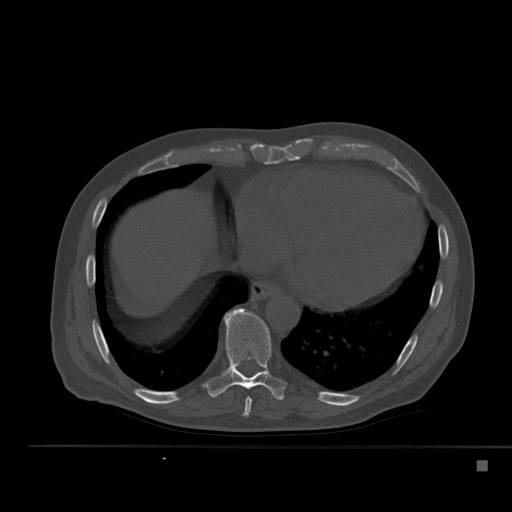
CT including the spine, one axial slice; position 290 of 517 along the scan axis; 120 kVp; bone window (W 1800 / L 400 HU); 1.5 mm slice thickness; 512 × 512 image matrix. Male patient, age 70 years. Case-level facts recorded for this patient, not image findings: primary cancer: renal; vertebrae with lytic lesions (as recorded): T4, T6, T10, T12, L3, L4, L5.
Annotated regions visible in this slice (semi-automatically segmented with operator editing):
- T8 vertebra: bounding box <243,397,252,417> (left, top, right, bottom; pixels)
- T9 vertebra: <206,308,287,400>